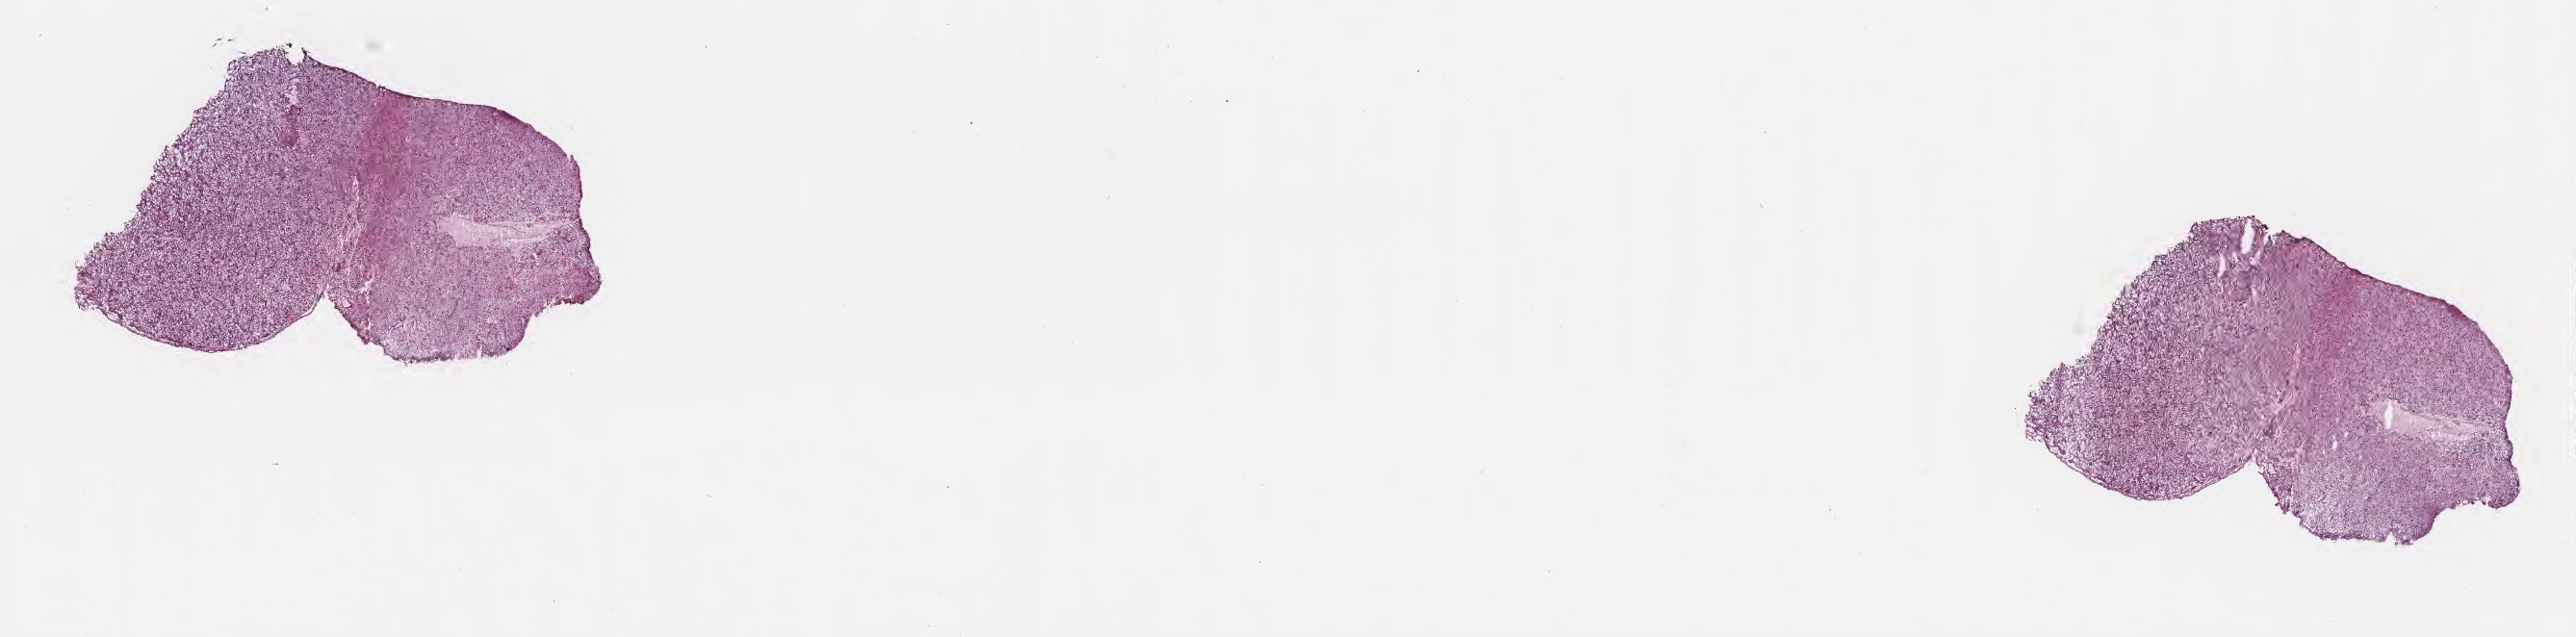
Haematoxylin and eosin whole-slide image, low-resolution overview of the scanned area, about 21.6 x 5.4 mm; frozen section; primary tumor; anatomic site: brain. Patient: male, age at initial diagnosis 49 years. Slide review estimates, as recorded: tumor cells 60%, tumor nuclei 82%, stromal cells 27%, necrosis 0%, normal cells 13%. Inflammatory infiltration, as recorded: lymphocyte infiltration 2%, monocyte infiltration 0%, neutrophil infiltration 0%.
Section: top of the tissue portion. Histologic diagnosis: Glioblastoma, NOS.